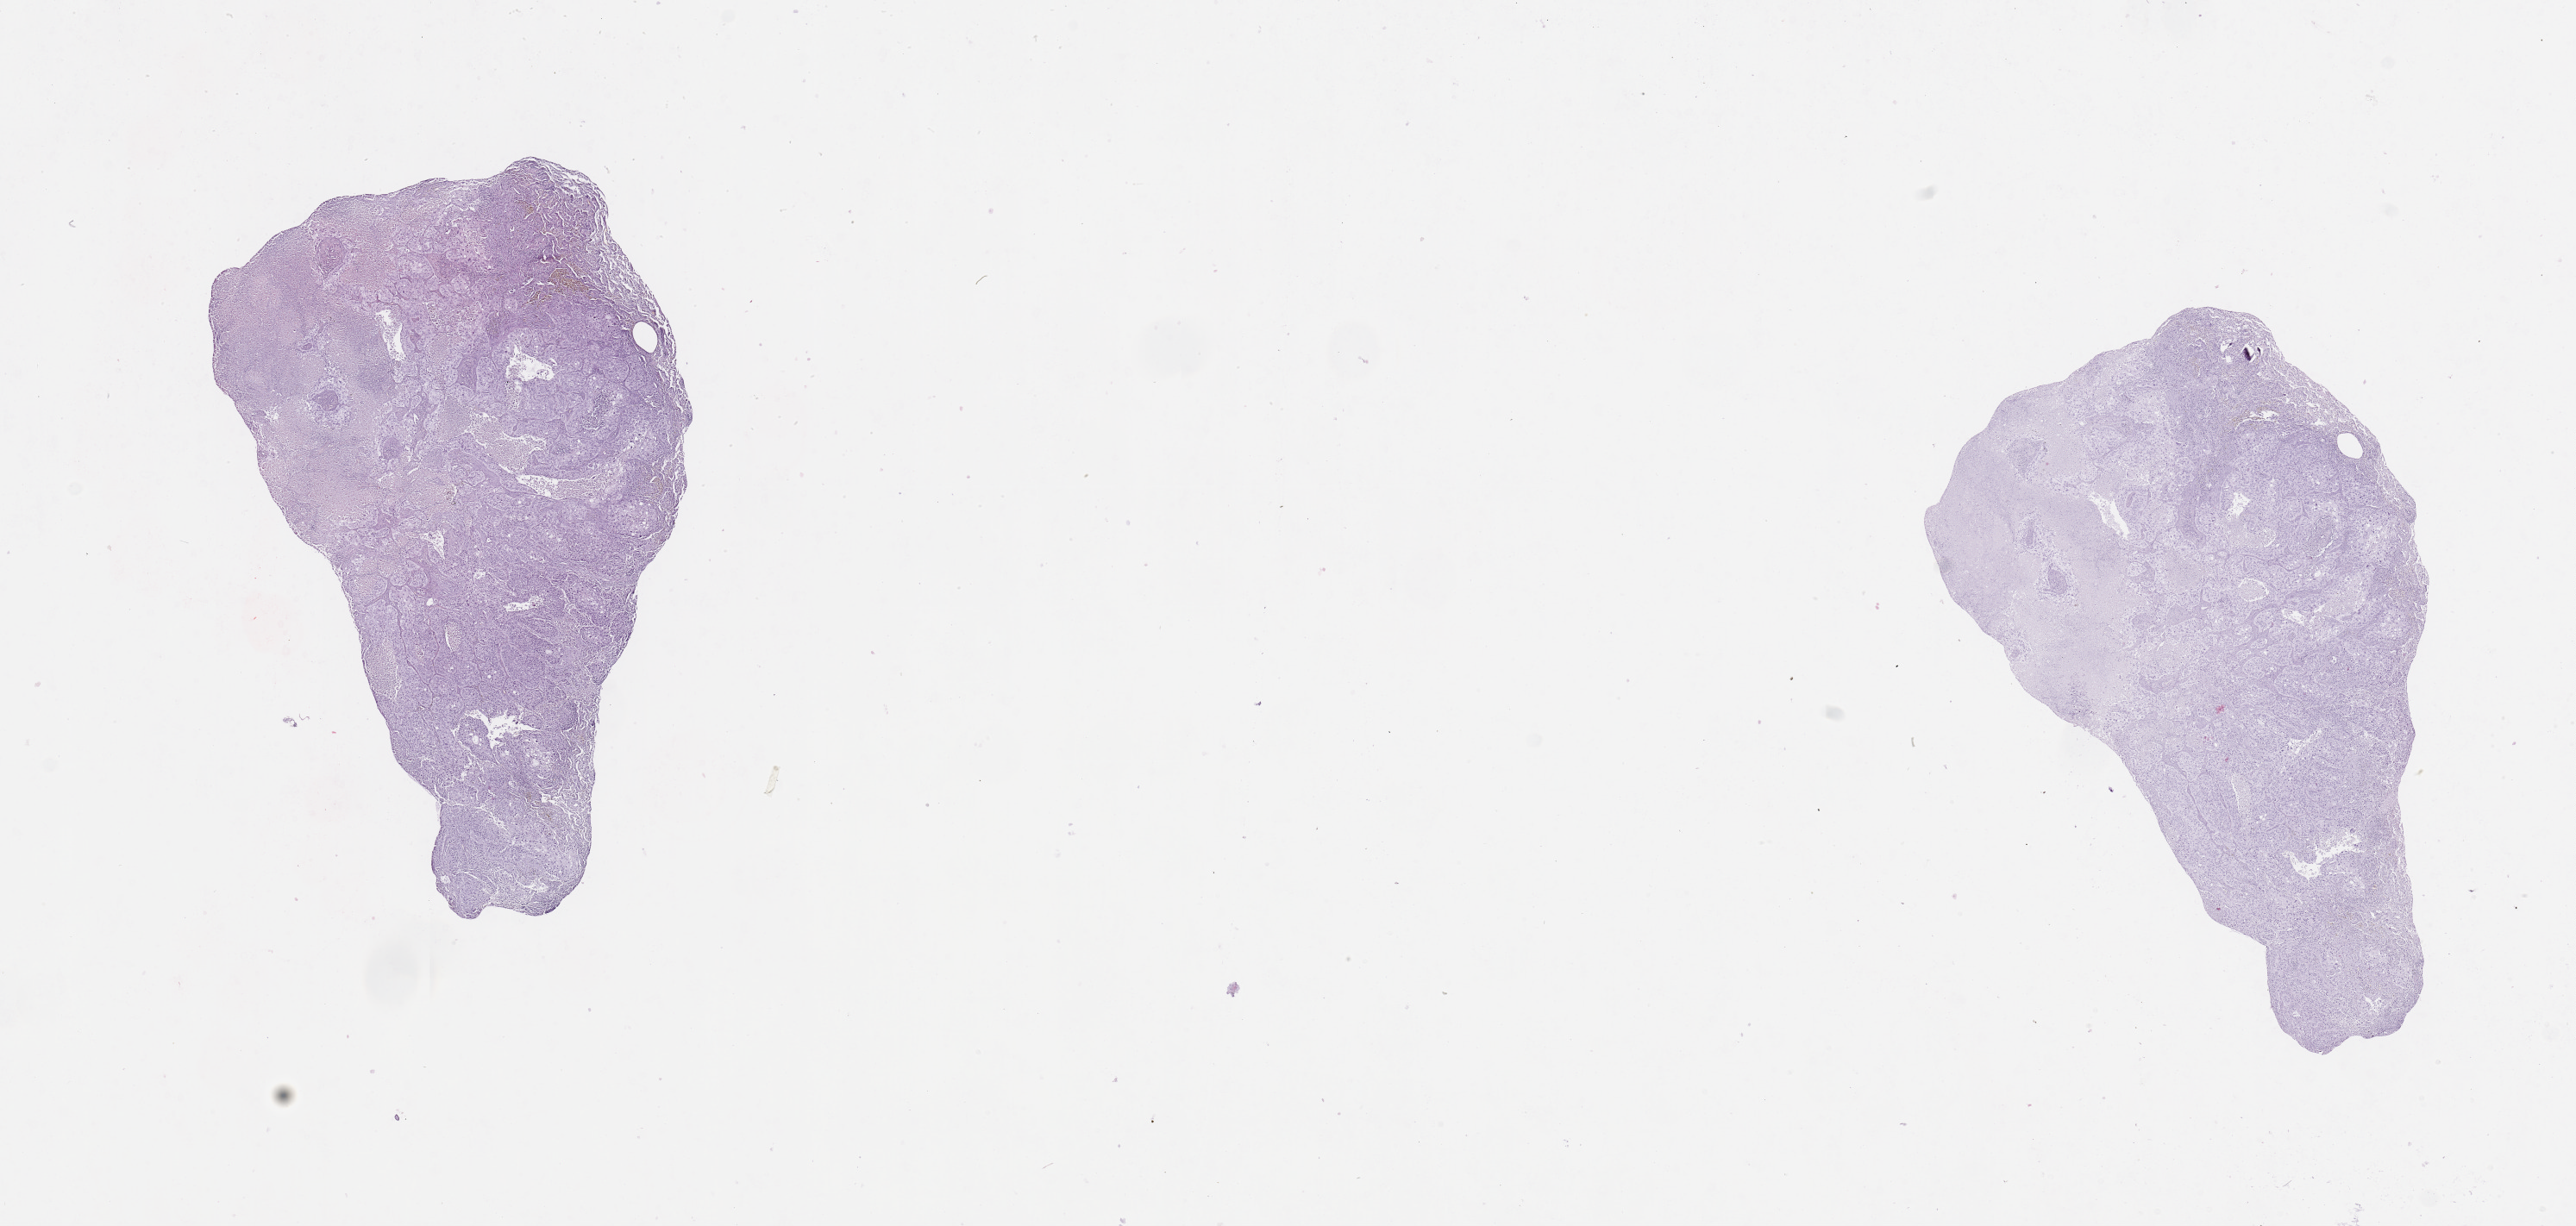
Digitized H&E-stained tissue section (whole slide) — low-resolution overview of the scanned area, about 23.6 x 11.2 mm (slide scanned at 20x), tumour tissue sample, sampled site: lung. 74-year-old male patient. Histologic grade: G2 (moderately differentiated). Slide review estimates, as recorded: tumour nuclei 60%, necrosis 20%.
AJCC pathologic stage: IIIA. Diagnosis: Squamous cell carcinoma, NOS. Primary tumour site (as recorded): left lower lobe.